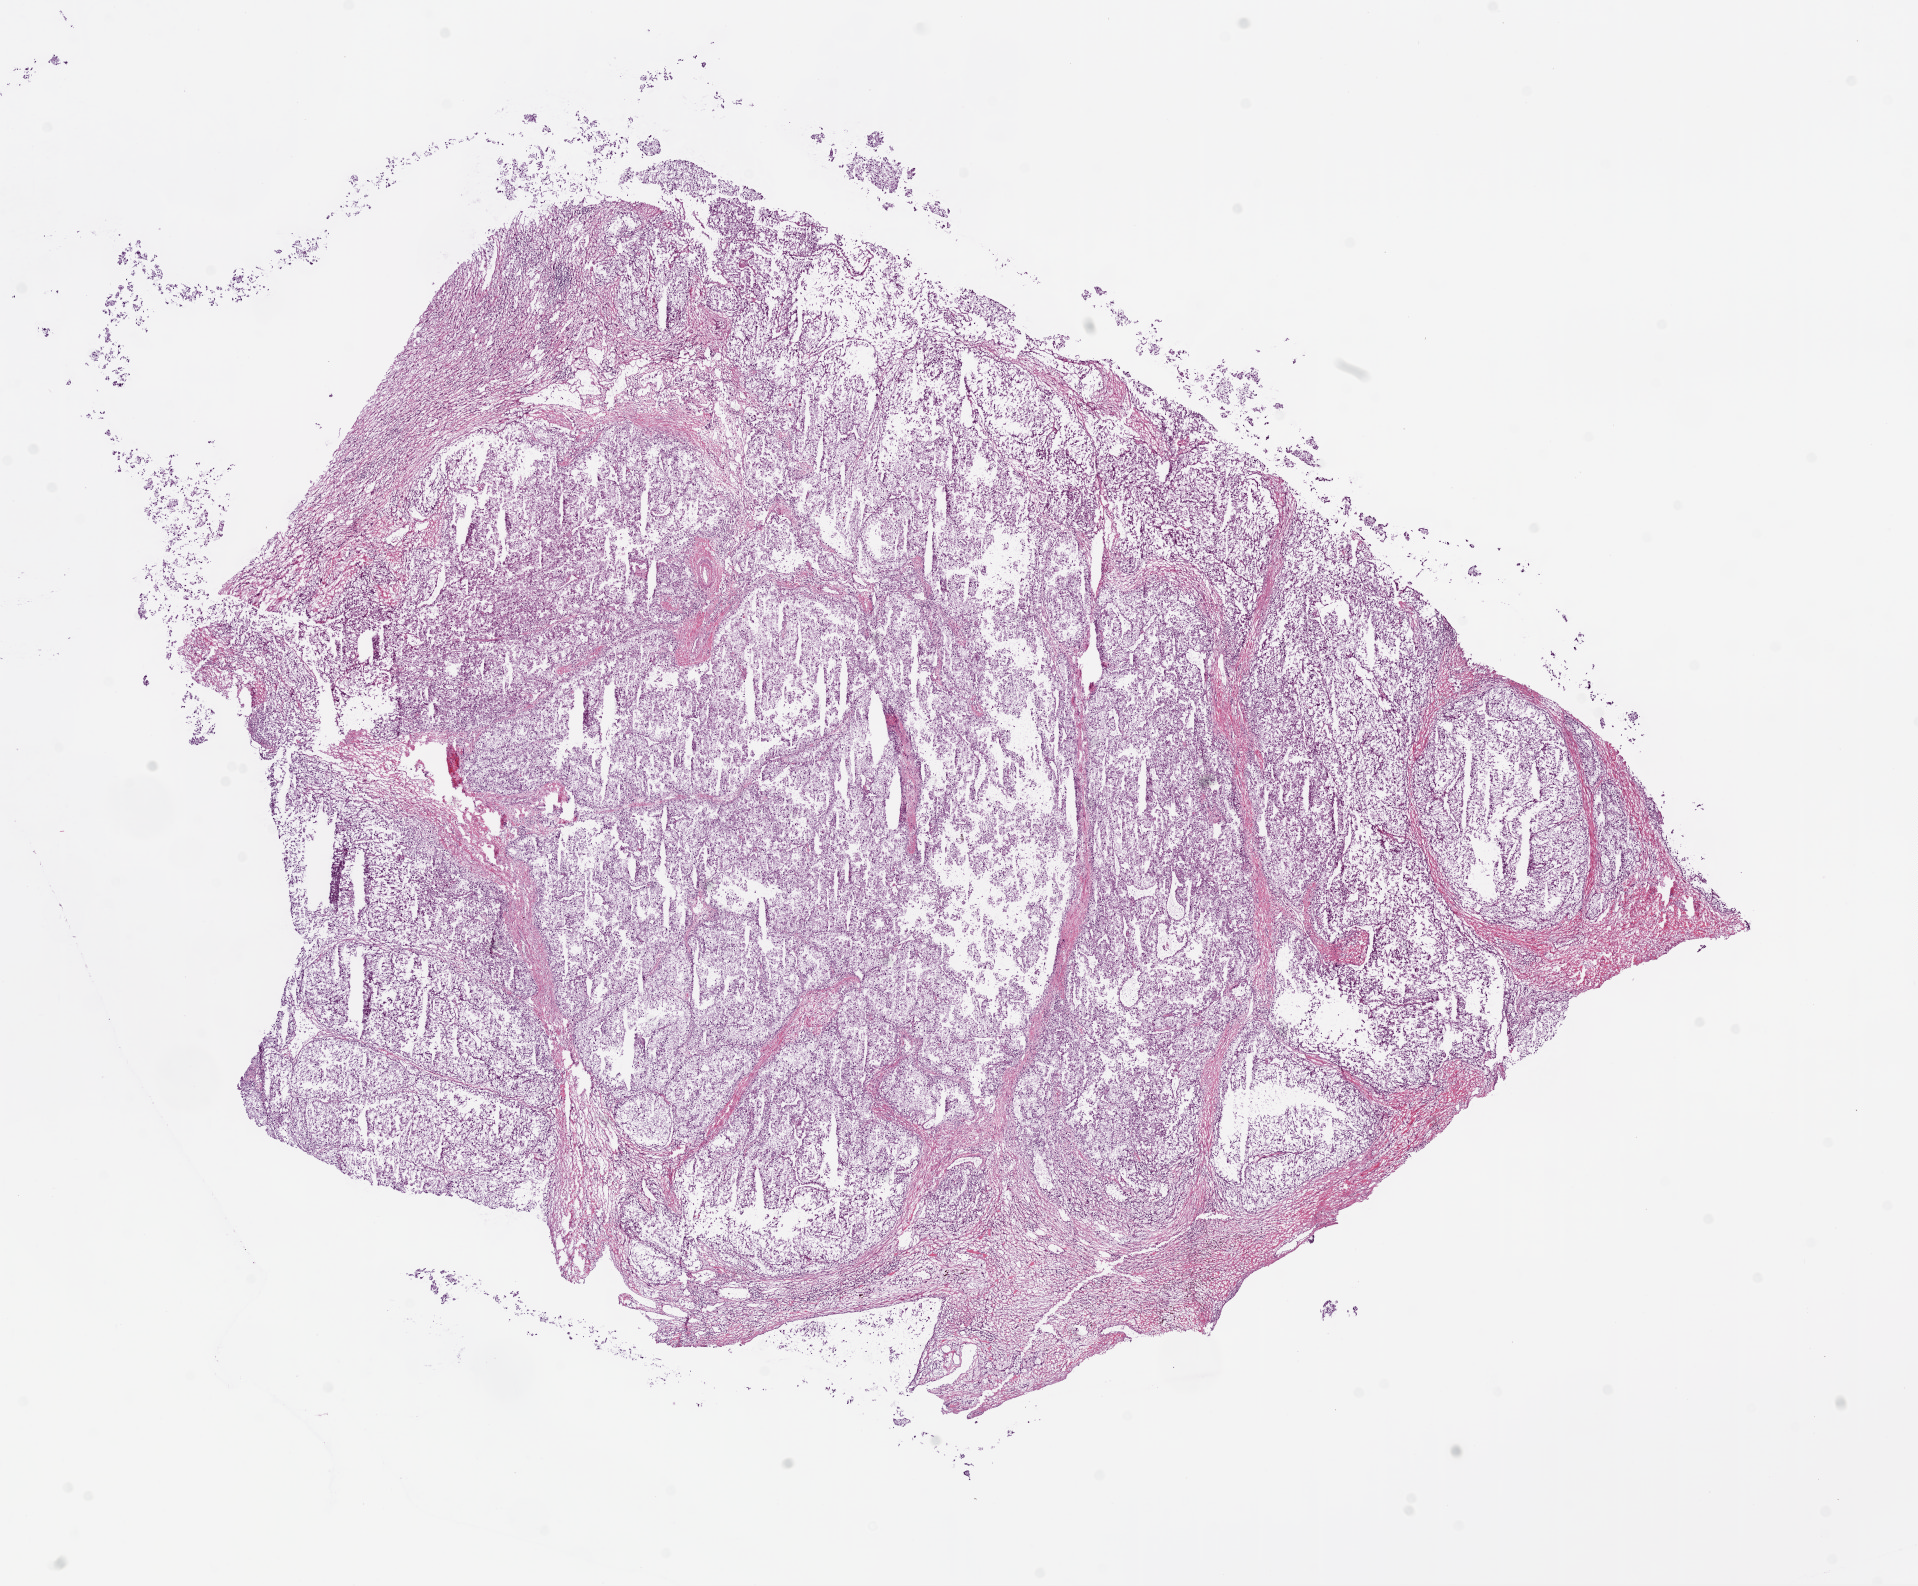
H&E whole-slide image — whole scanned area (about 15.5 x 12.8 mm) shown as a low-resolution overview. Frozen section from the bottom of the tissue portion. Primary tumour sample from the kidney. Patient: male, age at initial diagnosis 52 years. Histologic grade: G2 (moderately differentiated). Pathologist review of this section (percent, as recorded): tumour cells 90%, tumour nuclei 85%, normal cells 0%, stromal cells 10%, necrosis 0%. Inflammatory infiltration, as recorded: lymphocyte infiltration 1%, monocyte infiltration 0%, neutrophil infiltration 0%.
Diagnosis: Clear cell adenocarcinoma, NOS.